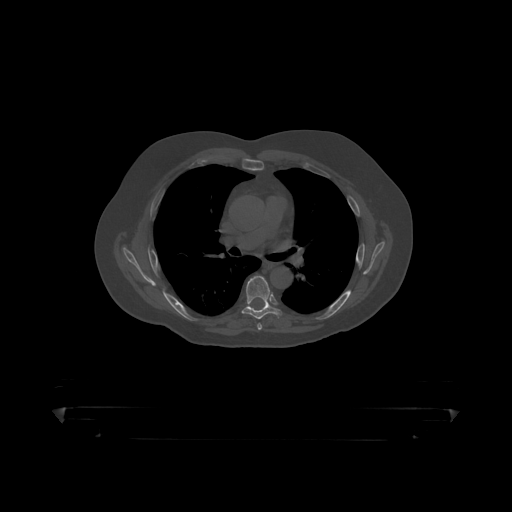
CT including the spine, one axial slice; slice 302 of 390 in the series (ordered by position); reconstruction kernel STANDARD; 120 kVp; bone window (W 1800 / L 400 HU); 1.25 mm slice thickness; 512 × 512 image matrix. Patient: male, 60 years. Case-level facts recorded for this patient, not image findings: primary cancer: prostate.
Structures marked on this image (semi-automatic segmentation, software-assisted and operator-edited):
- T6 vertebra: bounding box <242,277,281,319> (left, top, right, bottom; pixels)